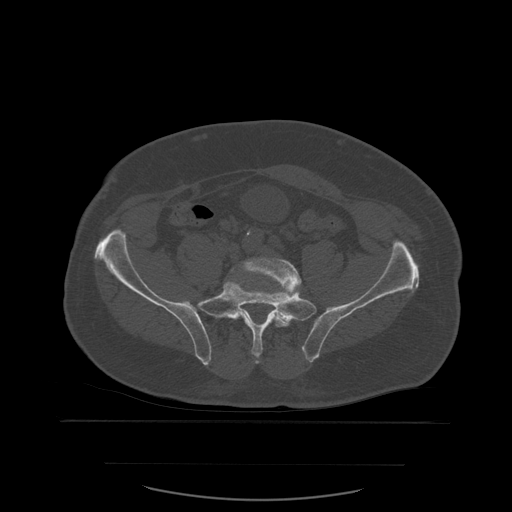
CT including the spine, one axial slice. Slice 123 of 590 in the series (ordered by position). Bone window (W 1800 / L 400 HU). 1.25 mm slice thickness. 512 × 512 image matrix, field of view 479 × 479 mm. Patient age 71 years. From the clinical record (not read from this slice): primary cancer: lung; vertebrae with lytic lesions (as recorded): T1, T2, L5, S1.
Outlined on this slice (semi-automatically segmented with operator editing):
- L5 vertebra: bounding box [x1, y1, x2, y2] px = [219, 258, 302, 358]